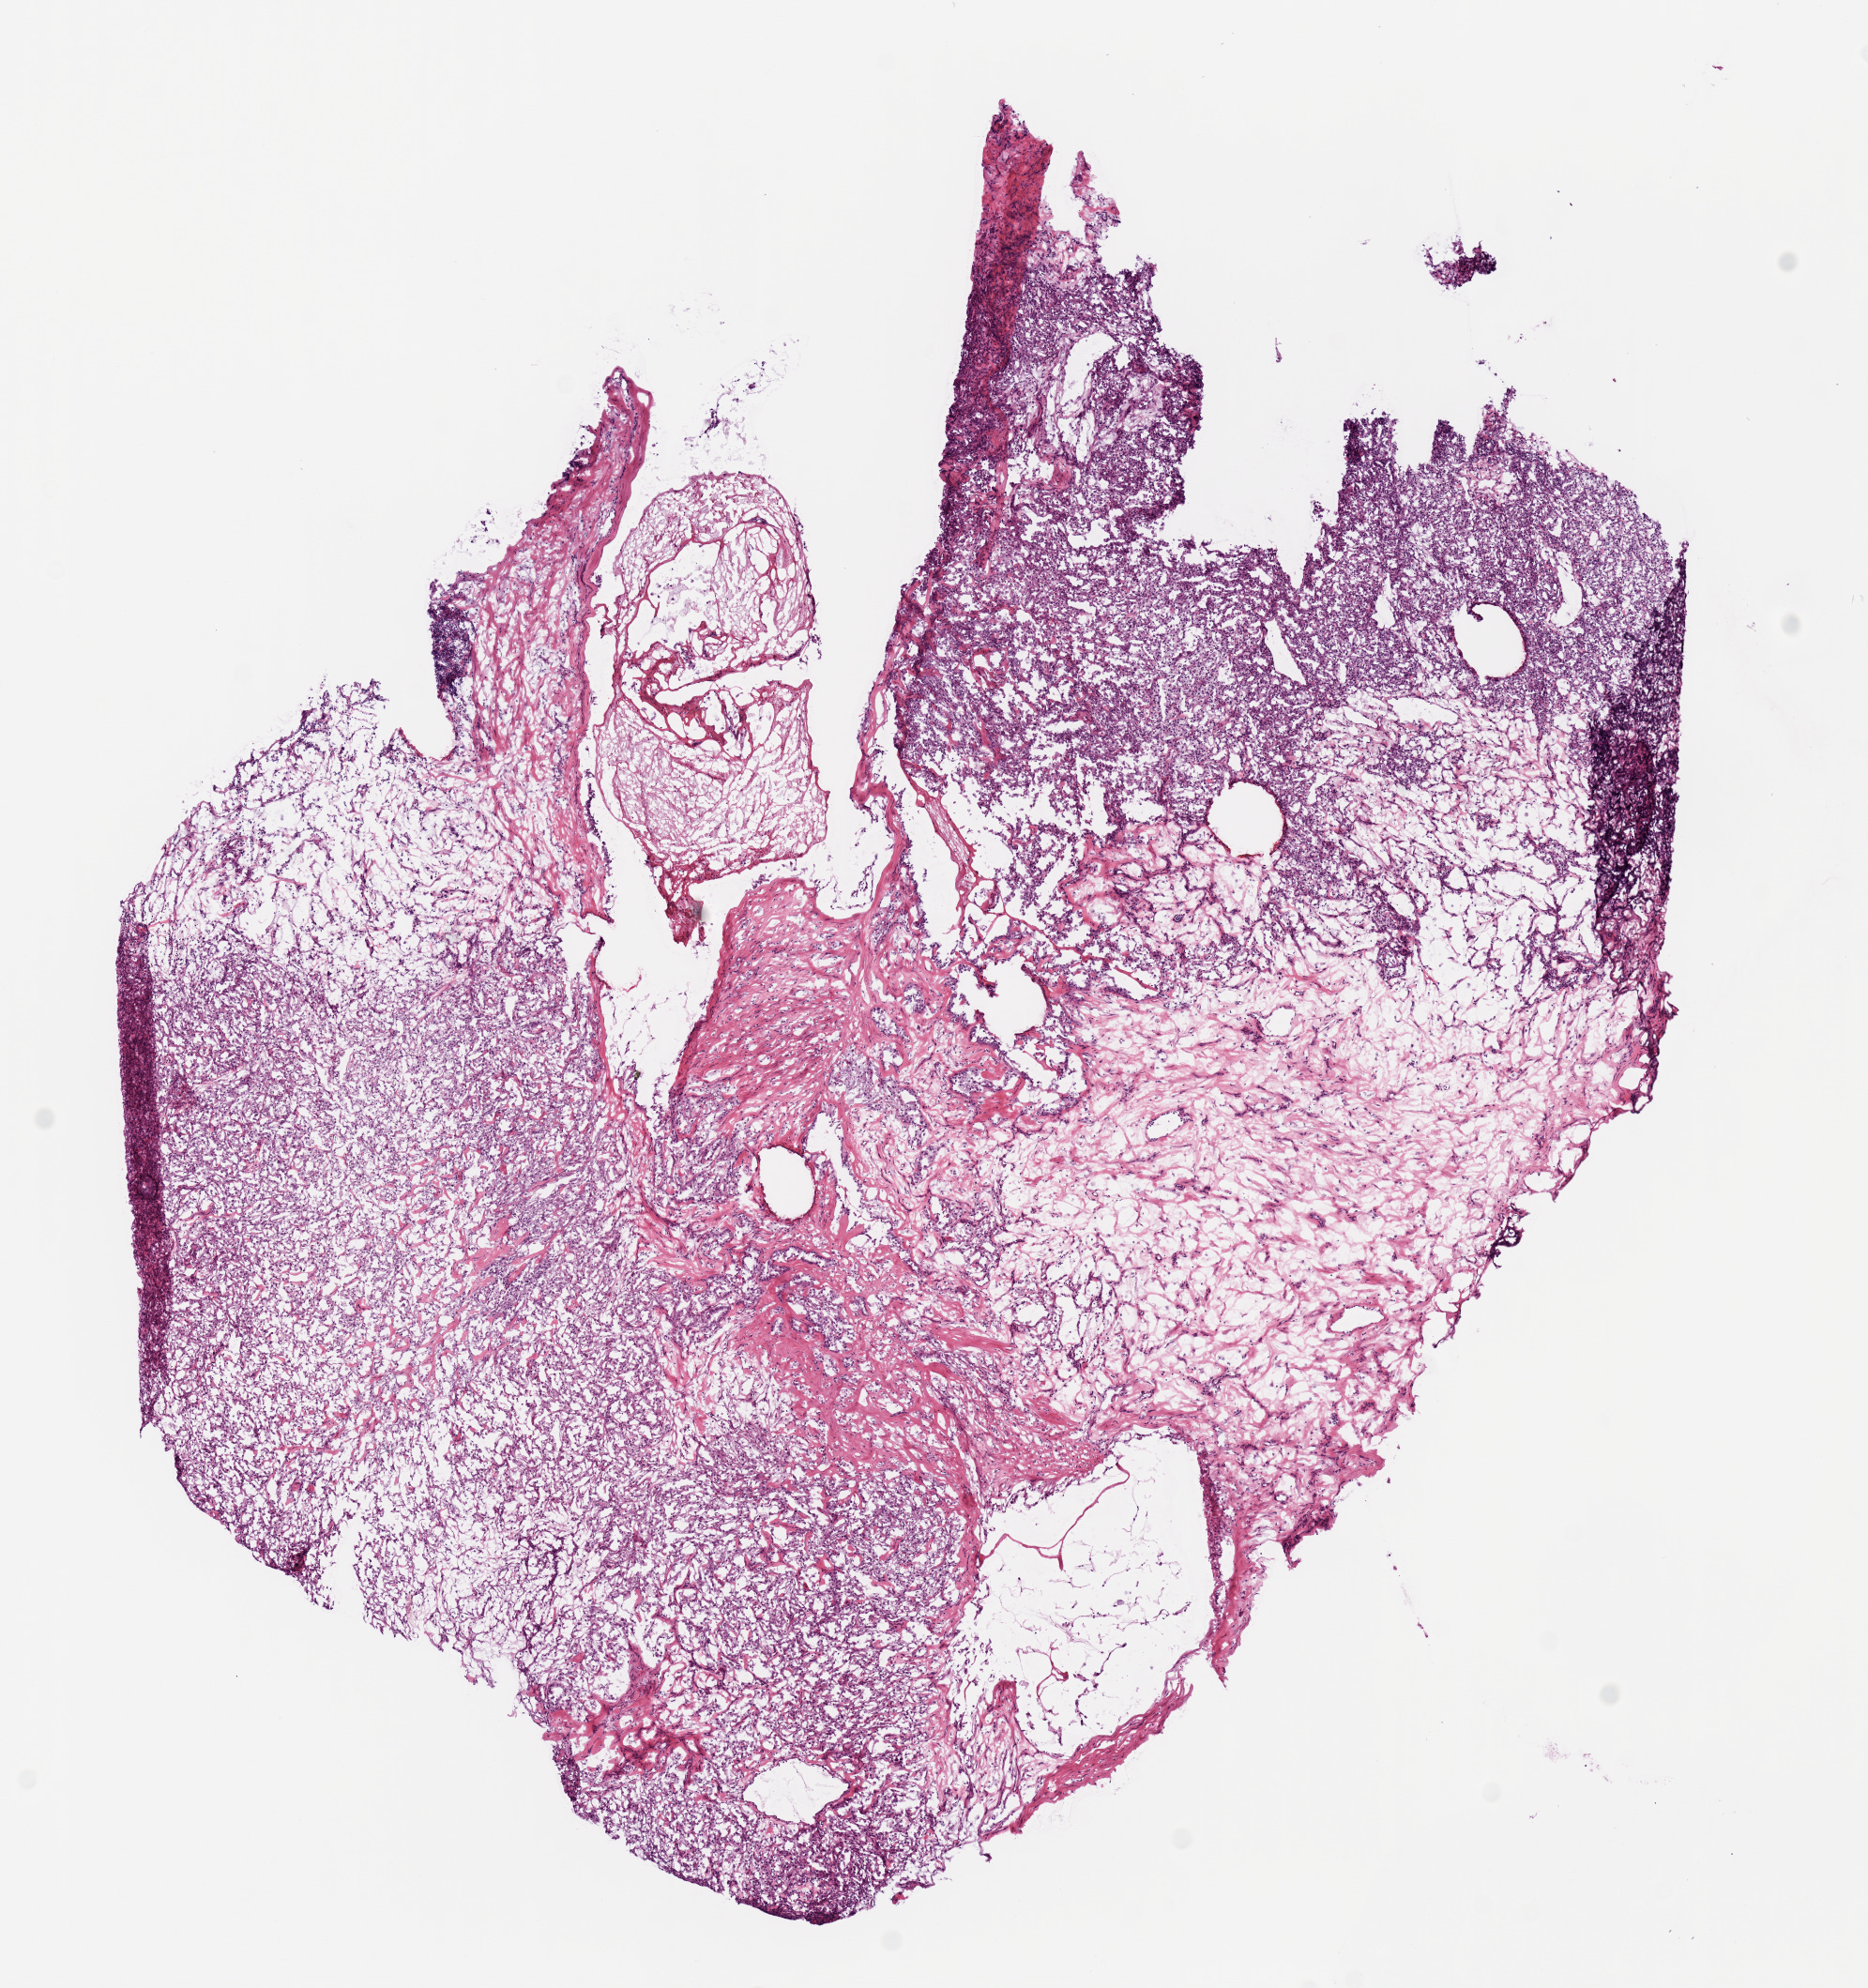
H&E-stained whole-slide image, shown as a low-resolution overview of the whole scanned area (about 7.9 x 8.4 mm, slide scanned at 20x). Frozen section. Sample: primary tumour, kidney. Patient: female, age at initial diagnosis 74 years. Pathologist review of this section (percent, as recorded): tumour cells 95%, tumour nuclei 80%, normal cells 0%, stromal cells 5%, necrosis 0%.
AJCC pathologic stage: I (7th edition). Histologic diagnosis: Papillary adenocarcinoma, NOS. Laterality: left.